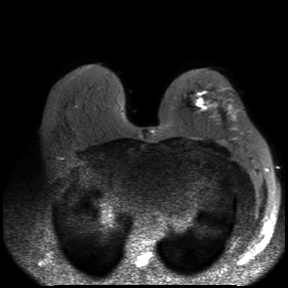
Breast MRI, one axial slice. Slice 19 of 30 in the series (ordered by position). Diffusion-weighted series; image 2 of 4 stored at this slice position (different b-values; order by instance number). 3 T. 4 mm slice thickness. 288 × 288 image matrix, field of view 360 × 360 mm. Female patient.
Structures marked on this image (outlined manually by an expert reader):
- tumour on diffusion-weighted imaging: box from (x=196, y=98) to (x=204, y=107) px